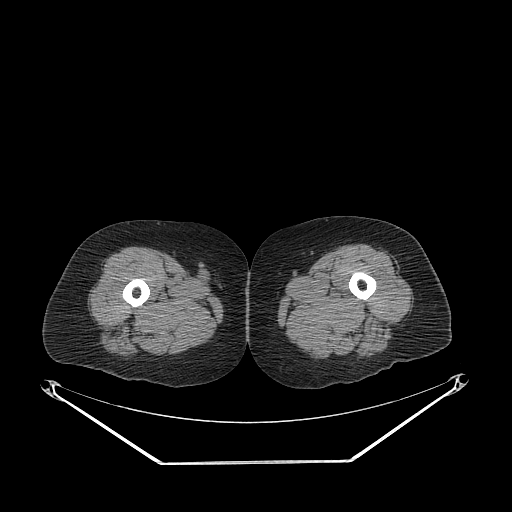
CT of an extremity soft-tissue mass (from a PET/CT study), one axial slice; position 246 of 311 along the scan axis; reconstruction kernel STANDARD; soft-tissue window (W 400 / L 40 HU); 512 × 512 image matrix, field of view 500 × 500 mm. Female patient. Case-level facts recorded for this patient, not image findings: histological type: leiomyosarcoma; grade: intermediate; site of the primary tumour: parascapusular.
Annotated regions visible in this slice (expert contour drawn on MRI and transferred to this co-registered scan by the dataset authors):
- gross tumour volume including surrounding oedema: bounding box <198,267,215,282> (left, top, right, bottom; pixels)
- gross tumour volume (mass): <199,267,211,280>